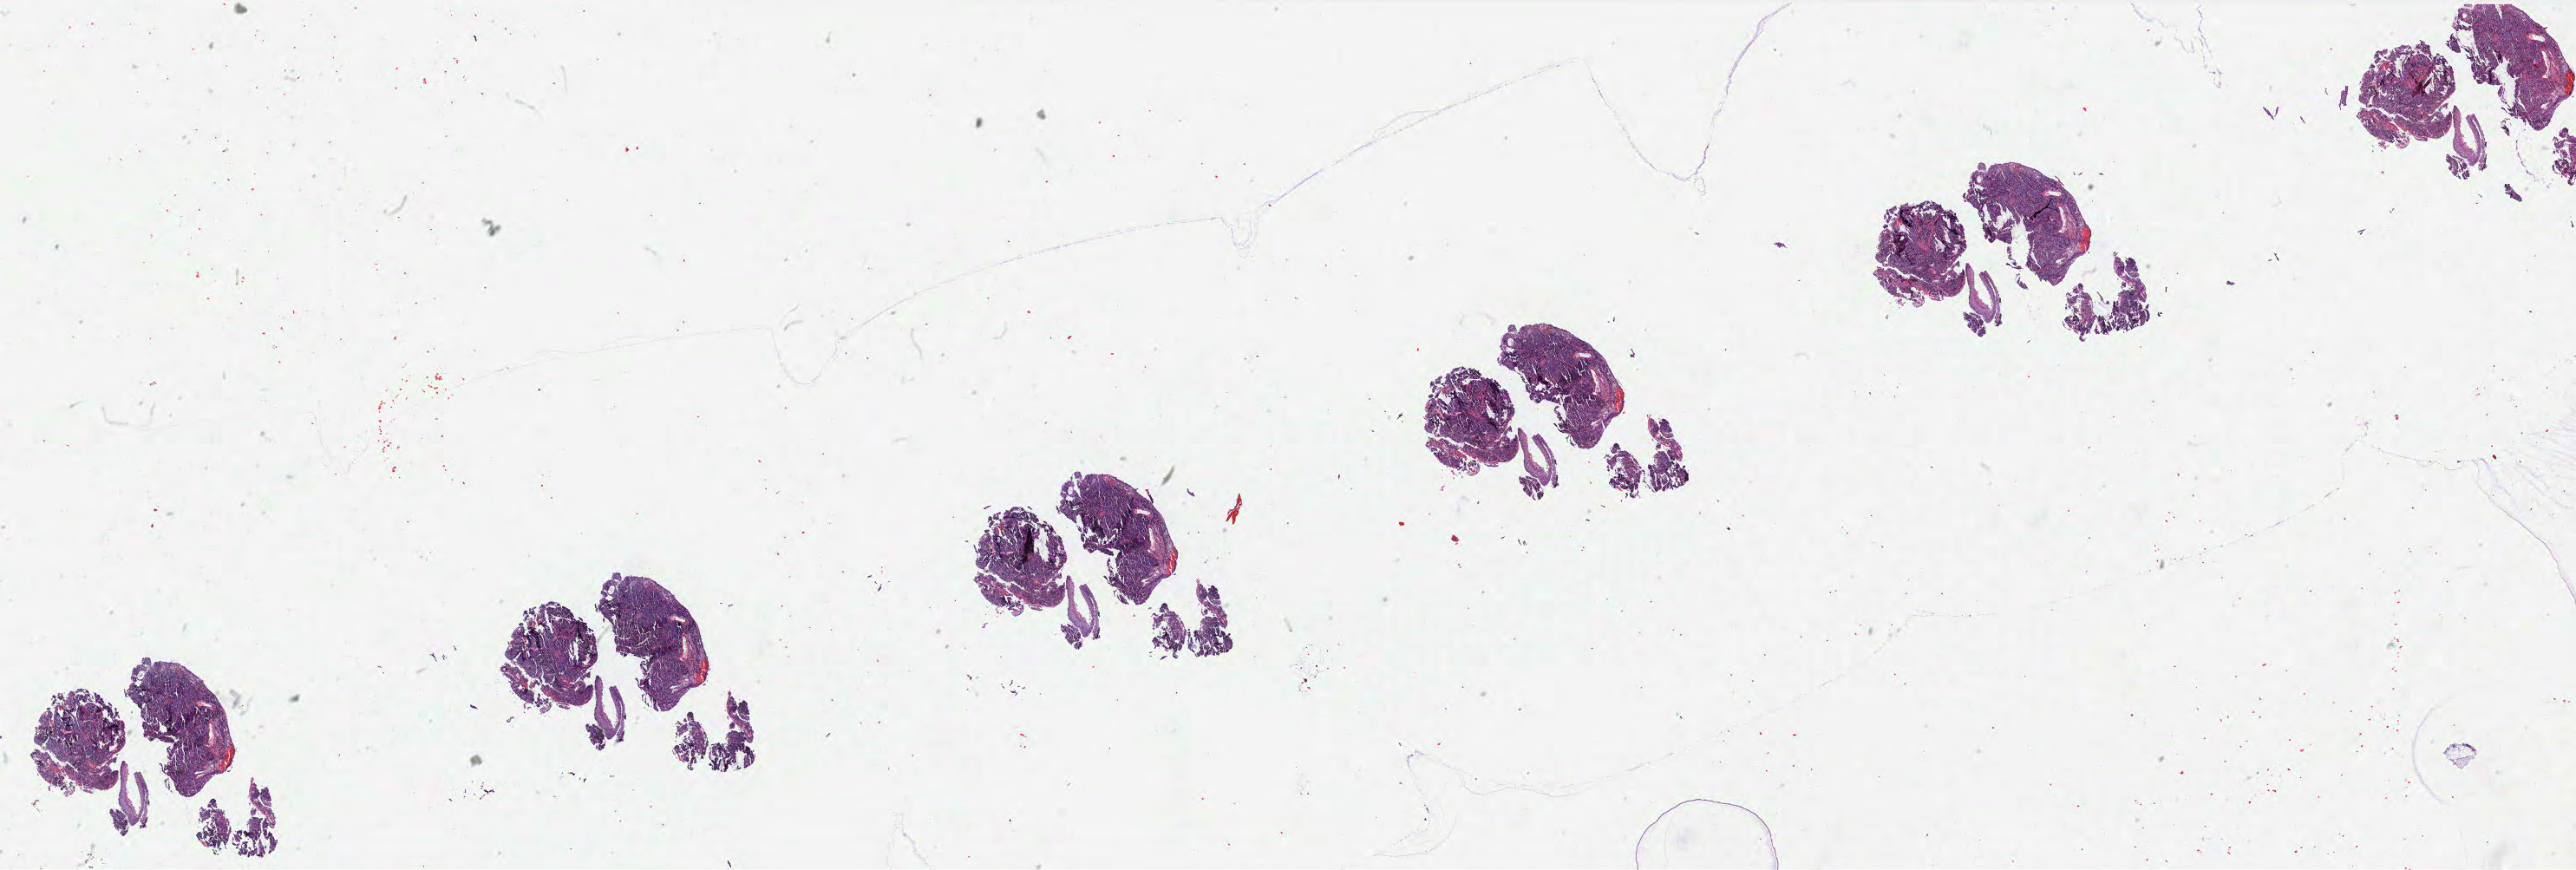
H&E-stained whole-slide image, shown as a low-resolution overview of the whole scanned area (about 47.5 x 16.1 mm, from a 40x scan). Formalin-fixed paraffin-embedded (FFPE) diagnostic section. Sample: primary tumour, cervix. Female, age 55 years at initial diagnosis. Histologic grade: G2 (moderately differentiated).
Lymph nodes positive (case pathology): 0 of 47 examined. FIGO stage: IB. Histologic diagnosis: Squamous cell carcinoma, NOS (cervix uteri).